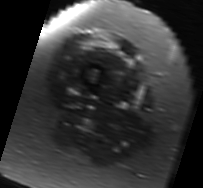
MRI of an extremity soft-tissue mass, one axial slice; slice 11 of 91 in the series (ordered by position); T2-weighted fat-saturated; MR volume resampled by the dataset authors to the PET/CT grid (not the native acquisition matrix); 3.27 mm slice thickness; 203 × 188 image matrix, field of view 198 × 184 mm. Female patient. From the clinical record (not read from this slice): histological type: malignant solitary fibrous tumor; grade: intermediate; site of the primary tumour: right thigh.
Outlined on this slice (expert contour drawn on MRI and transferred to this co-registered scan by the dataset authors):
- gross tumour volume including surrounding oedema: box from (x=88, y=37) to (x=134, y=66) px